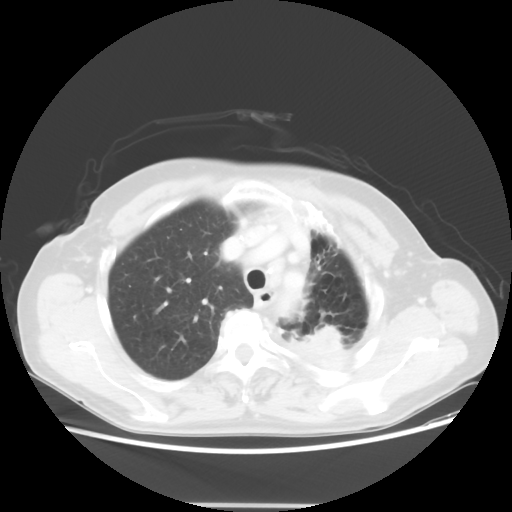
Chest CT, one axial slice. Slice 42 of 56 in the series (ordered by position). Reconstruction kernel STANDARD. Lung window (W 1500 / L -600 HU). 5 mm slice thickness. 512 × 512 image matrix, field of view 377 × 377 mm. Patient: female, 63 years. From the clinical record (not read from this slice): clinical TNM (as recorded): T2a N0 M0.
Annotated regions visible in this slice (rectangle marked by the reading radiologist):
- lung tumour (recorded histology: adenocarcinoma): bounding box [x1, y1, x2, y2] px = [305, 318, 342, 361]